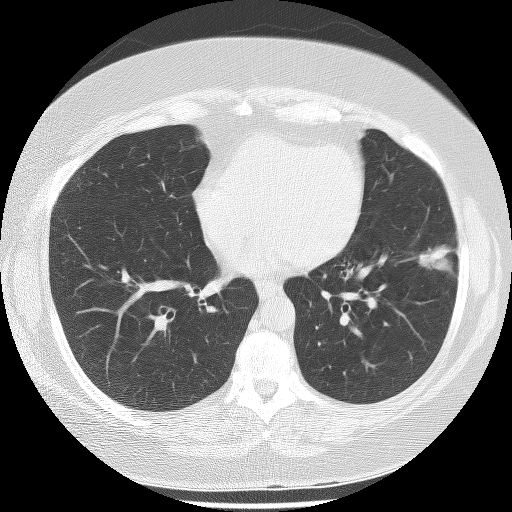
Low-dose screening chest CT, one axial slice. Position 107 of 233 along the scan axis. 120 kVp. Lung window (W 1500 / L -600 HU). 512 × 512 image matrix.
Outlined on this slice (expert manual segmentation):
- lesion 1 (tumor, lower lobe of left lung): bounding box (x1, y1, x2, y2) in pixels: (414, 244, 453, 274)